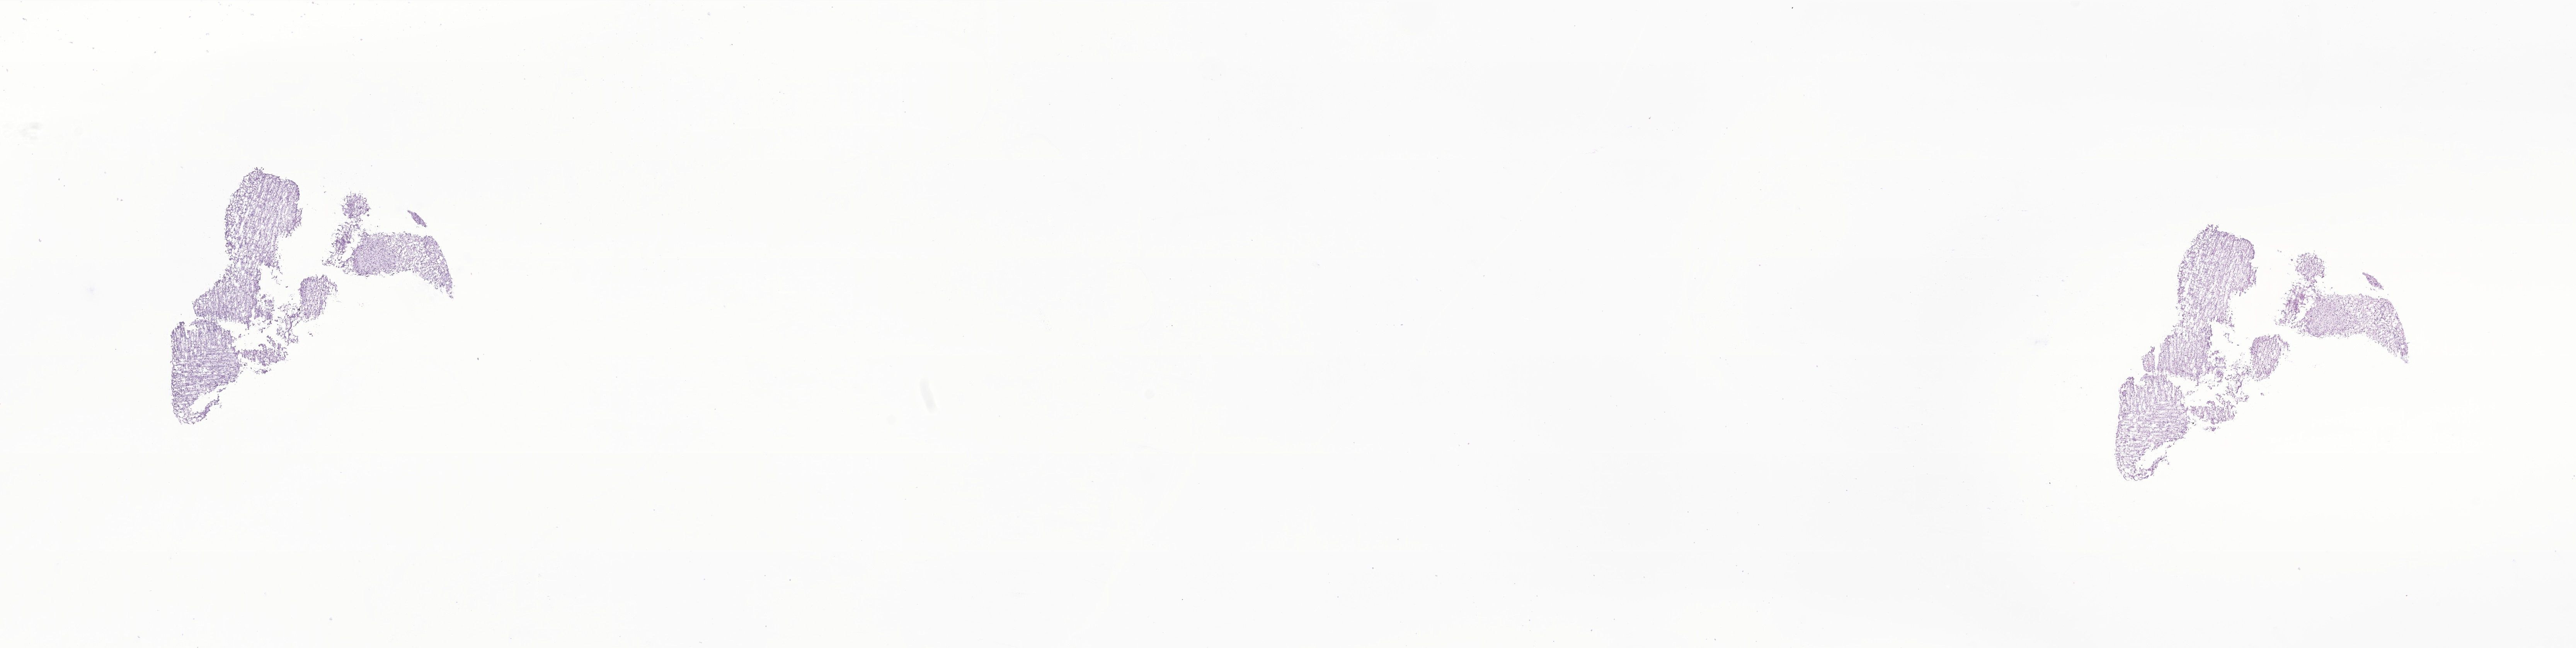
Hematoxylin and eosin (H&E) whole-slide image of tumor tissue from the brain, low-resolution overview of the scanned area, about 28.1 x 7.1 mm; cryosection (OCT / tissue freezing medium). Patient female; age 162 months (13 years 6 months).
Diagnosis (ICD-O-3 morphology term): Glioma, malignant.